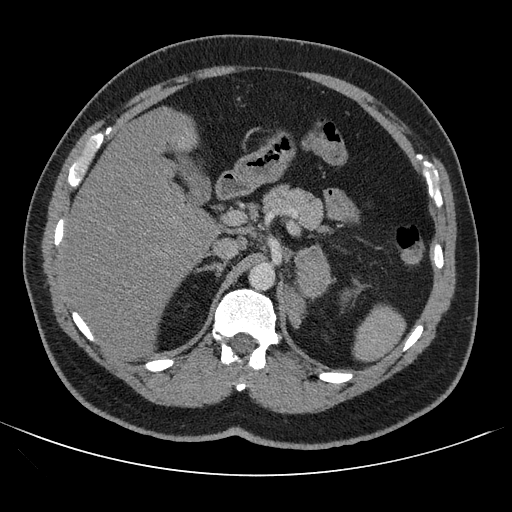
Contrast-enhanced abdominal CT, one axial slice; slice 68 of 121 in the series (ordered by position); 120 kVp; intravenous contrast given; soft-tissue window (W 400 / L 40 HU); 2.5 mm slice thickness; 512 × 512 image matrix, field of view 399 × 399 mm. Patient: male, 53 years. From the clinical record (not read from this slice): diagnosis: adrenocortical carcinoma; tumour side: left adrenal; tumour size at pathology: 7.9 cm; Ki-67 index: 20 %; stage (as recorded): 2.
Outlined on this slice (semi-automatic segmentation, software-assisted and operator-edited):
- mass: bounding box (x1, y1, x2, y2) in pixels: (287, 248, 329, 325)